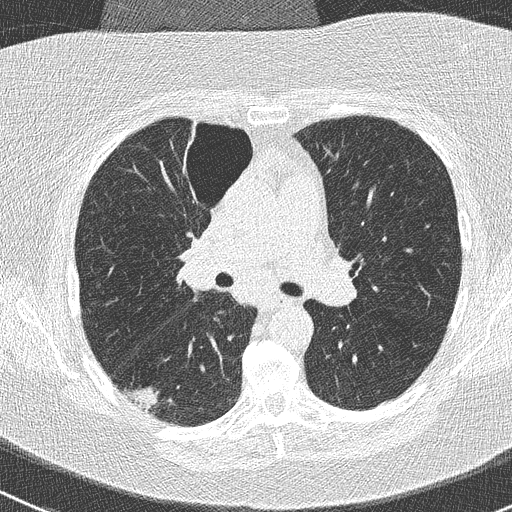
Low-dose screening chest CT, one axial slice; position 159 of 261 along the scan axis; reconstruction kernel B50f; lung window (W 1500 / L -600 HU); 2 mm slice thickness; 512 × 512 image matrix, field of view 310 × 310 mm.
Structures marked on this image (outlined manually by an expert reader):
- lesion 1 (tumor, lower lobe of right lung): bounding box (x1, y1, x2, y2) in pixels: (126, 387, 159, 410)